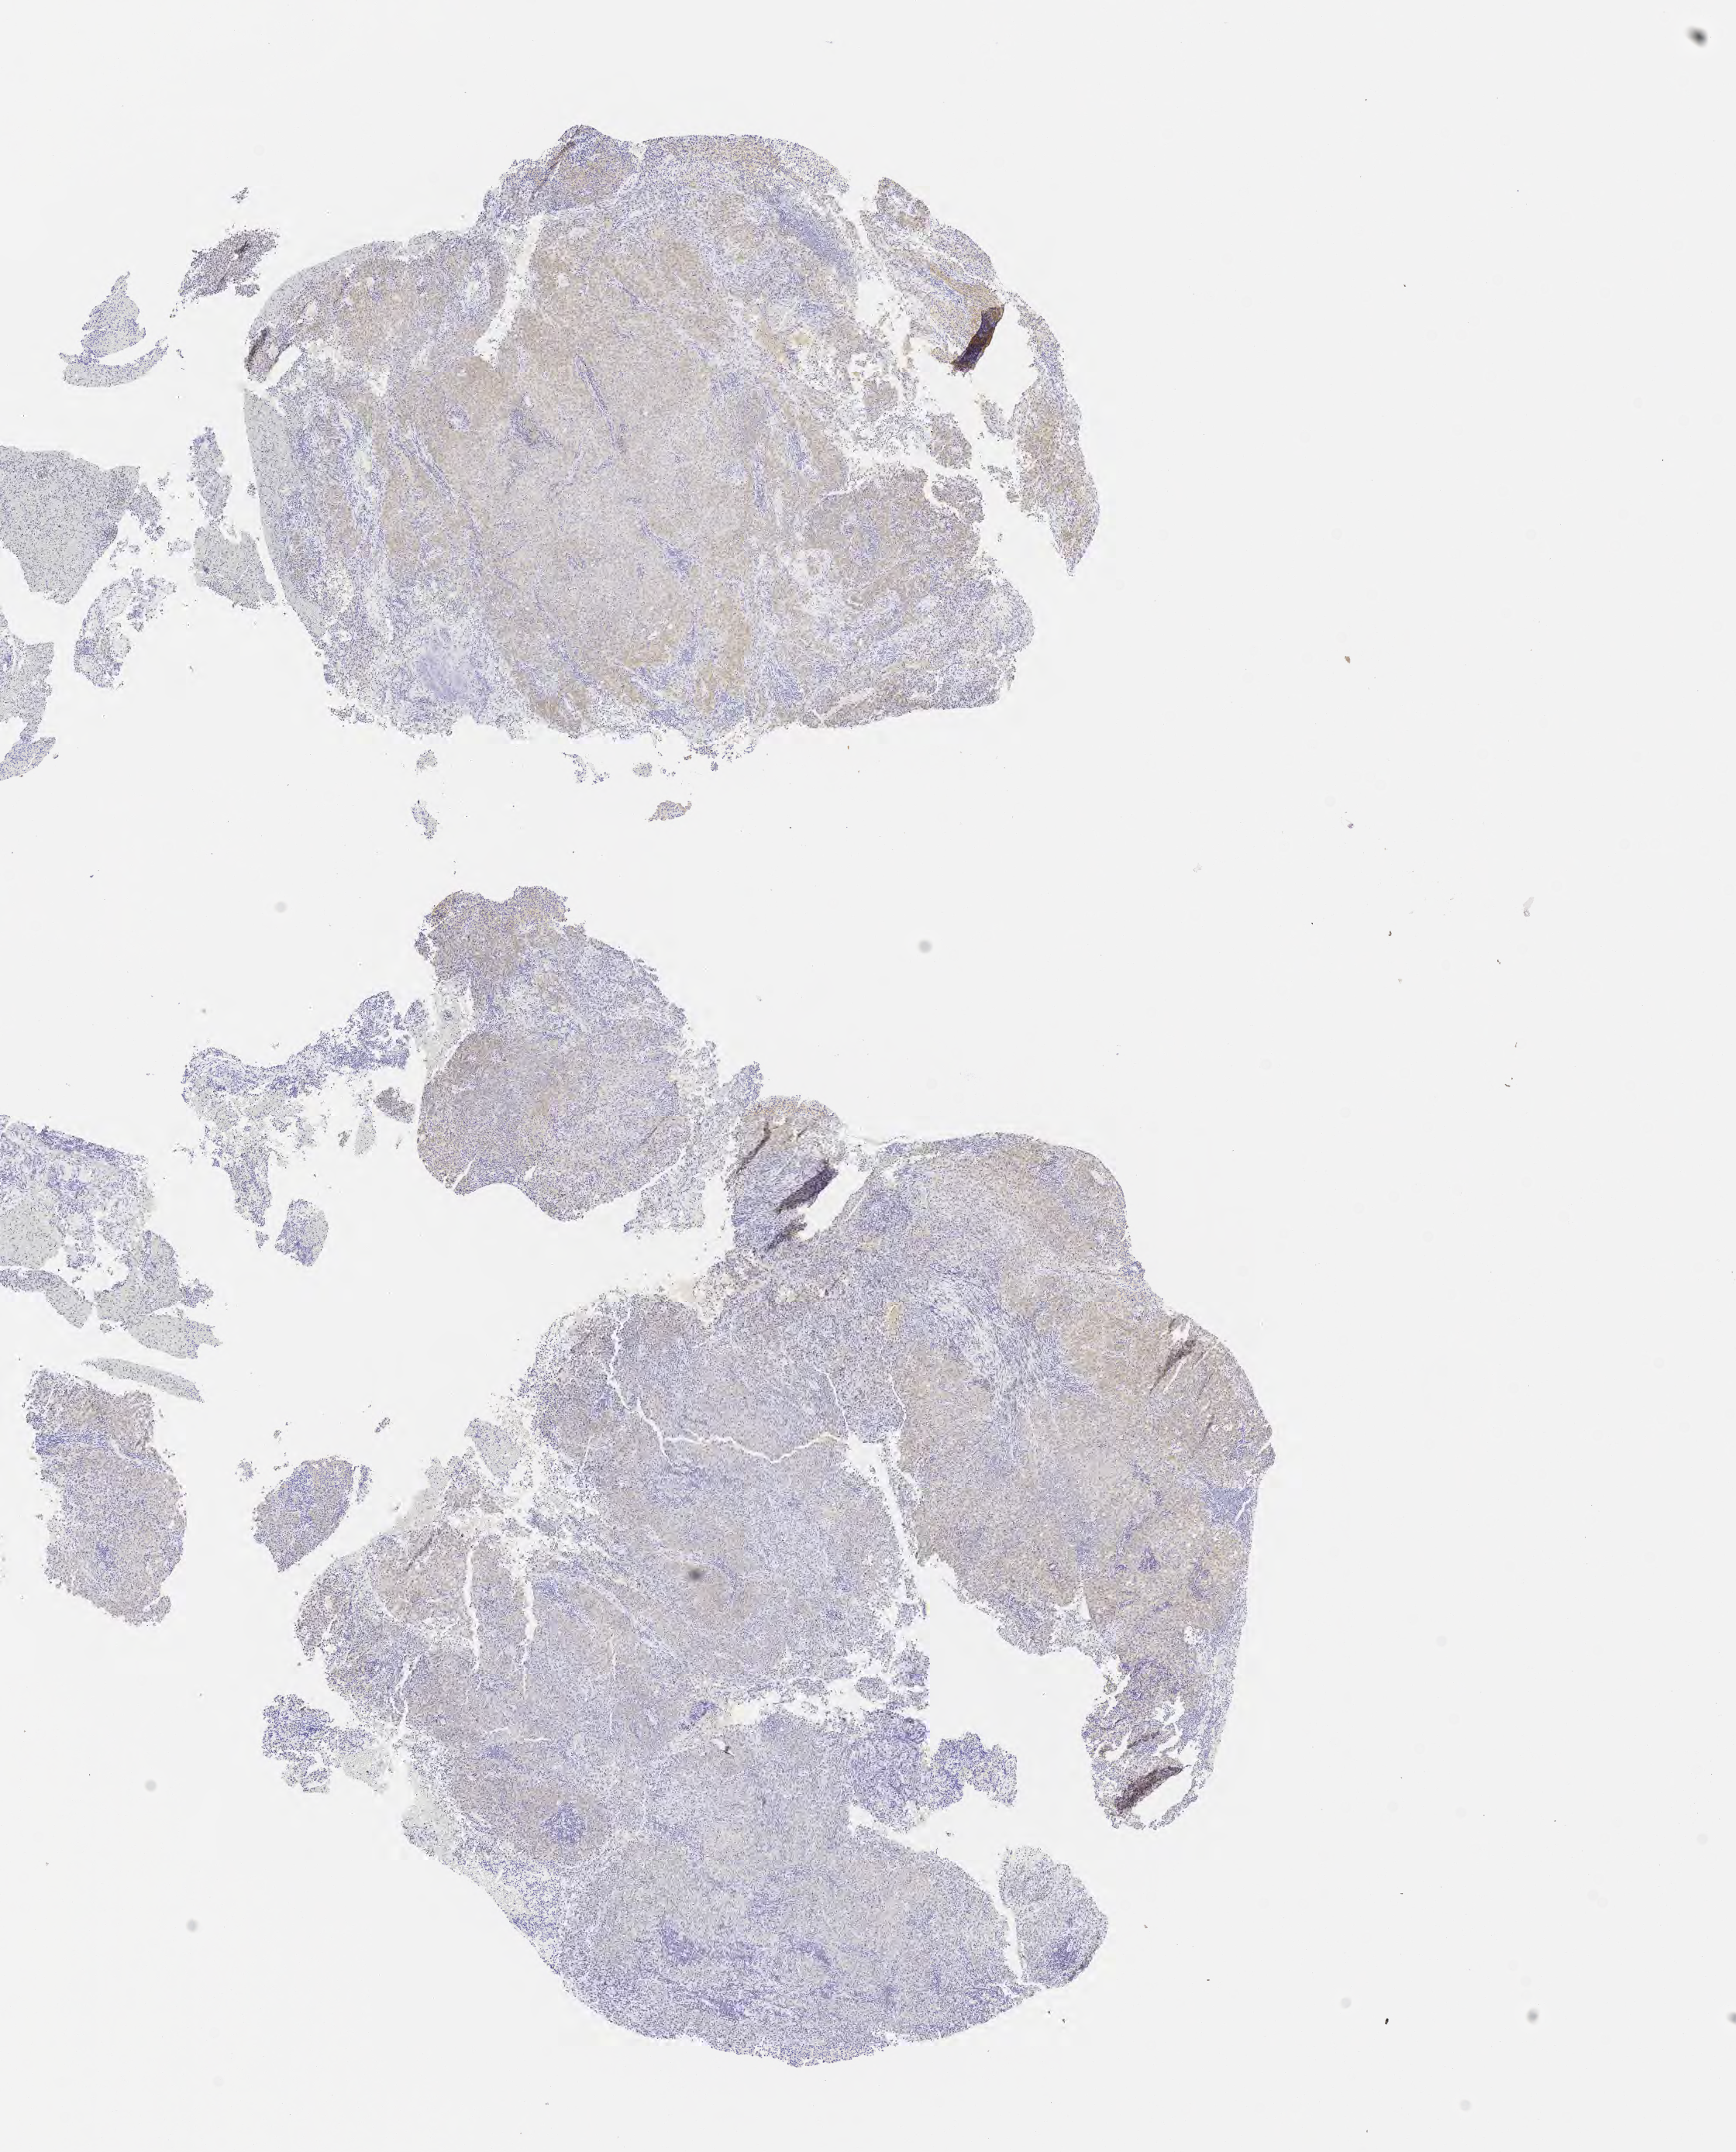
IHC for p63, whole-slide image — shown as a low-resolution overview of the whole scanned area (about 9.1 x 11.2 mm), tumor tissue, site: cervix. Patient female; aged 70.
Histologic diagnosis: Squamous cell carcinoma, large cell, nonkeratinizing, NOS.